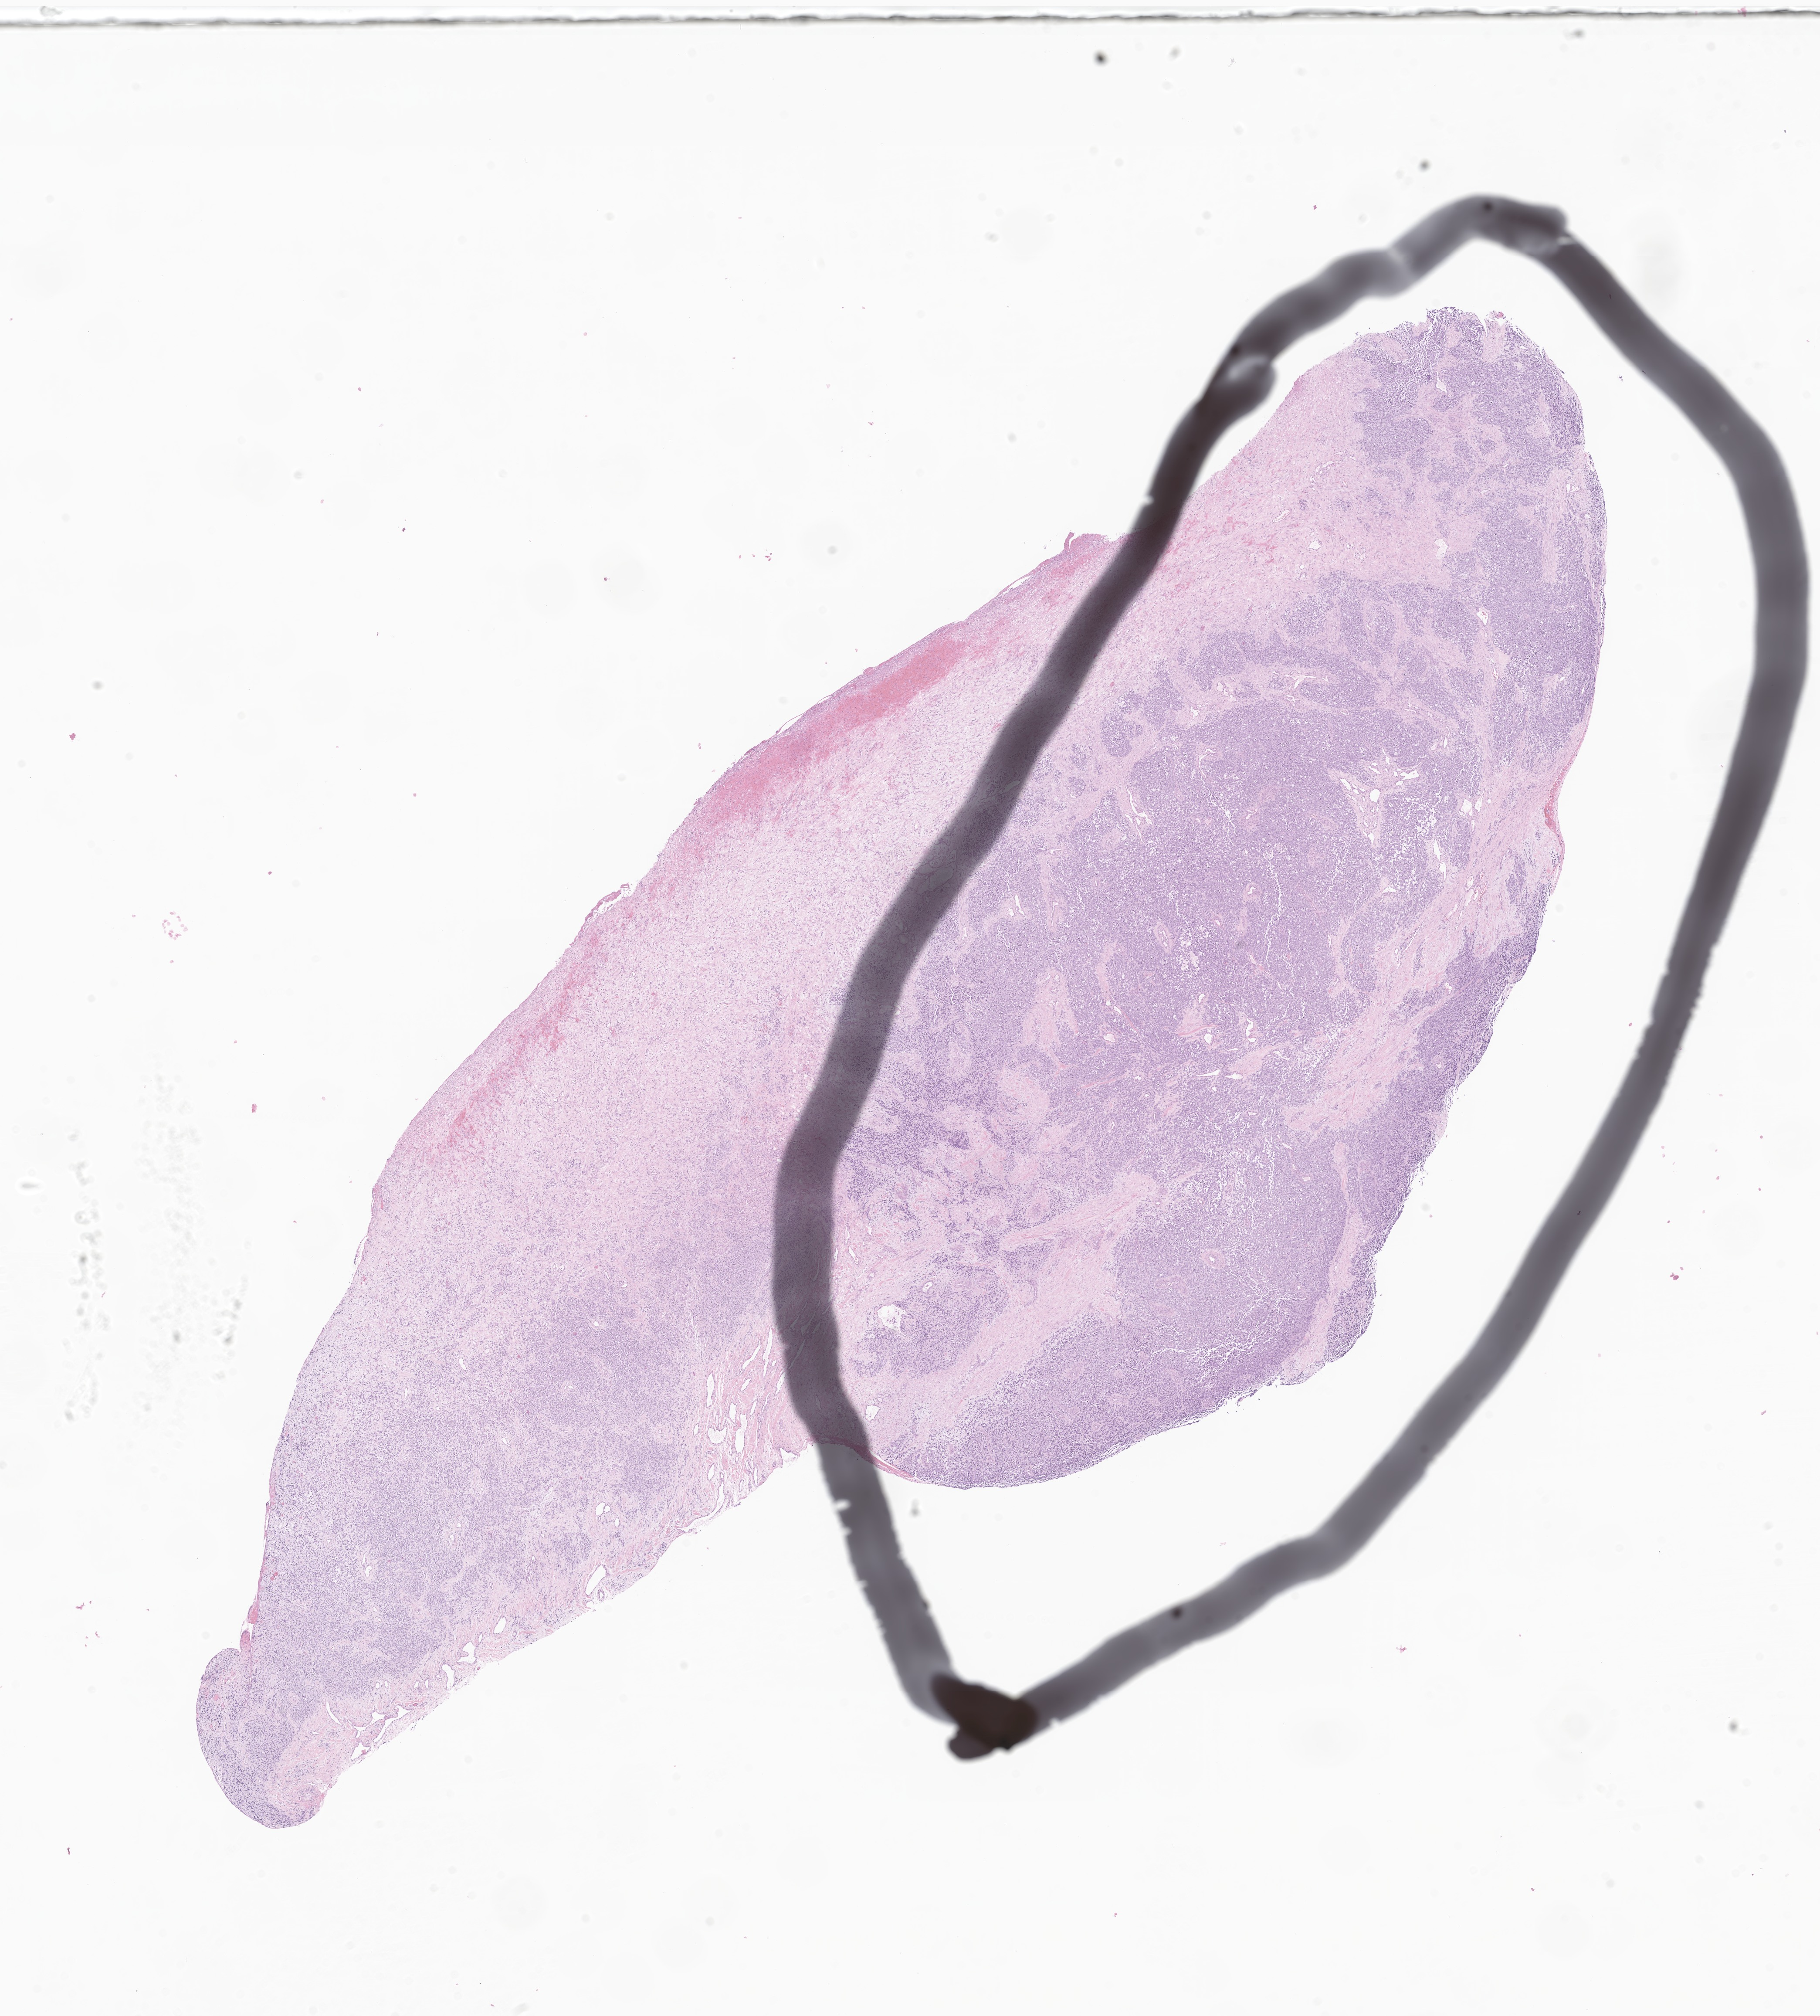
Digitized hematoxylin and eosin (H&E)-stained section of tumor tissue from the urinary bladder, a low-resolution overview of the entire scanned area, about 17.6 x 19.5 mm; FFPE section. Patient: male, age 49 months (4 years 1 month).
Diagnosis (ICD-O-3 morphology term): Alveolar rhabdomyosarcoma.